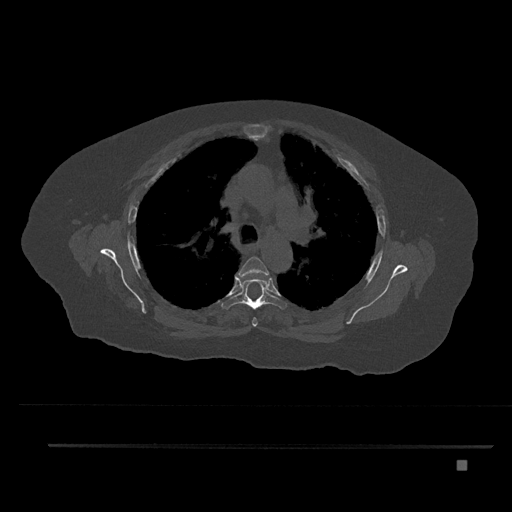
CT including the spine, one axial slice; slice 578 of 797 in the series (ordered by position); reconstruction kernel Br40s/3; bone window (W 1800 / L 400 HU); 512 × 512 image matrix, field of view 437 × 437 mm. Patient: female, 76 years. Case-level facts recorded for this patient, not image findings: primary cancer: lung; vertebrae with lytic lesions (as recorded): T11, L3.
Annotated regions visible in this slice (semi-automatic segmentation, software-assisted and operator-edited):
- T4 vertebra: box from (x=236, y=257) to (x=269, y=327) px
- T5 vertebra: (x=221, y=278)–(x=287, y=310)